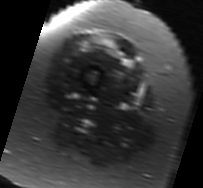
MRI of an extremity soft-tissue mass, one axial slice; position 12 of 91 along the scan axis; T2-weighted fat-saturated; MR volume resampled by the dataset authors to the PET/CT grid (not the native acquisition matrix); 203 × 188 image matrix. Female patient. From the clinical record (not read from this slice): histological type: malignant solitary fibrous tumor; grade: intermediate; site of the primary tumour: right thigh.
Outlined on this slice (expert contour drawn on MRI and transferred to this co-registered scan by the dataset authors):
- gross tumour volume including surrounding oedema: bounding box <86,37,134,68> (left, top, right, bottom; pixels)